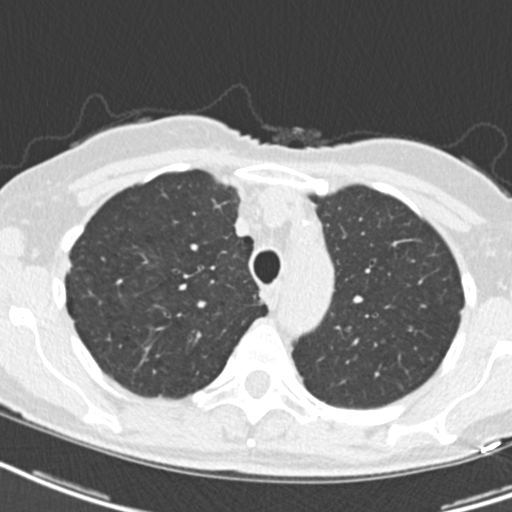
Chest CT (low-dose screening protocol), one axial image; first (baseline) screen; lung window (W 1500 / L -600 HU); slice 54 of 207 in the series. Female, age 68 years at enrolment.
Lesion marked by an expert reader, bounding box (x1, y1, x2, y2) in pixels: (247, 285, 271, 315). Screening reader's record for this exam: no non-calcified nodule ≥4 mm recorded. Official screen result: negative screen, no significant abnormalities.